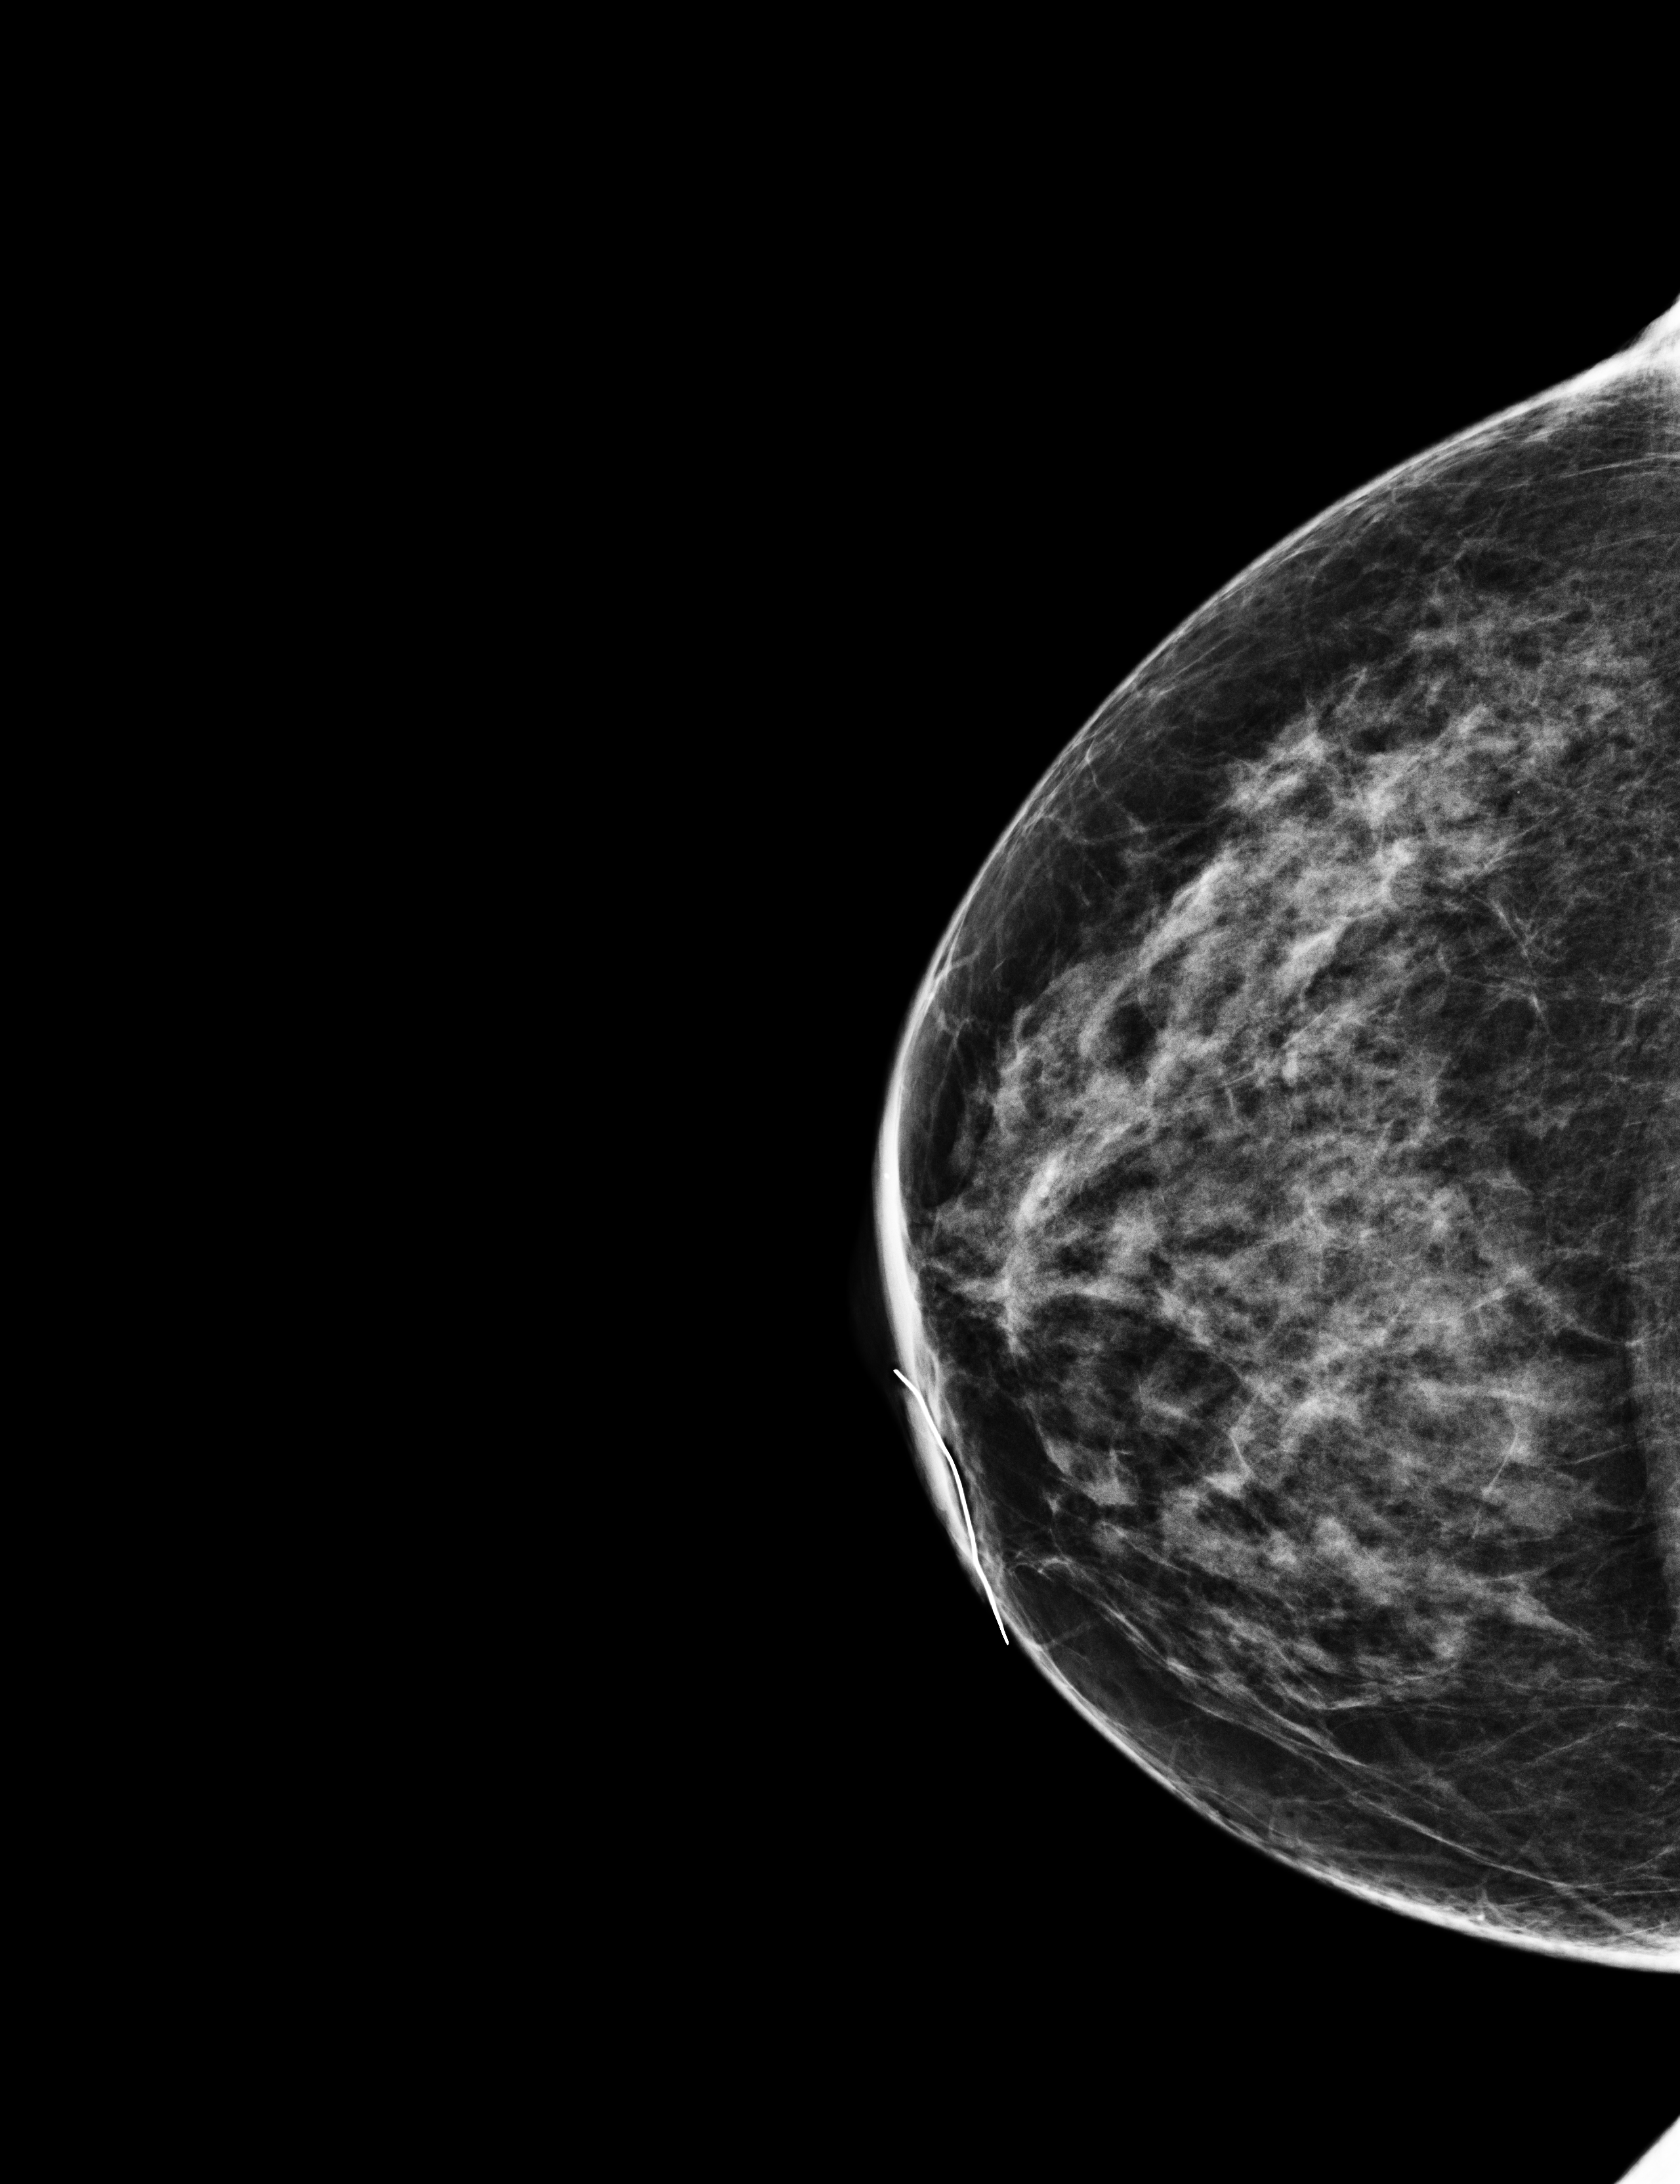
Full-field digital mammogram (FFDM); right breast; craniocaudal (CC) view; annual screening mammography examination; compressed breast thickness 57 mm; system: Selenia Dimensions. Patient: female, 60 years.
BI-RADS breast density category at the screening exam (both breasts, scale 1–4): 3. Final BI-RADS category for the screening round (tomosynthesis exam, both breasts): category 1. Recall: no recall after this screen.